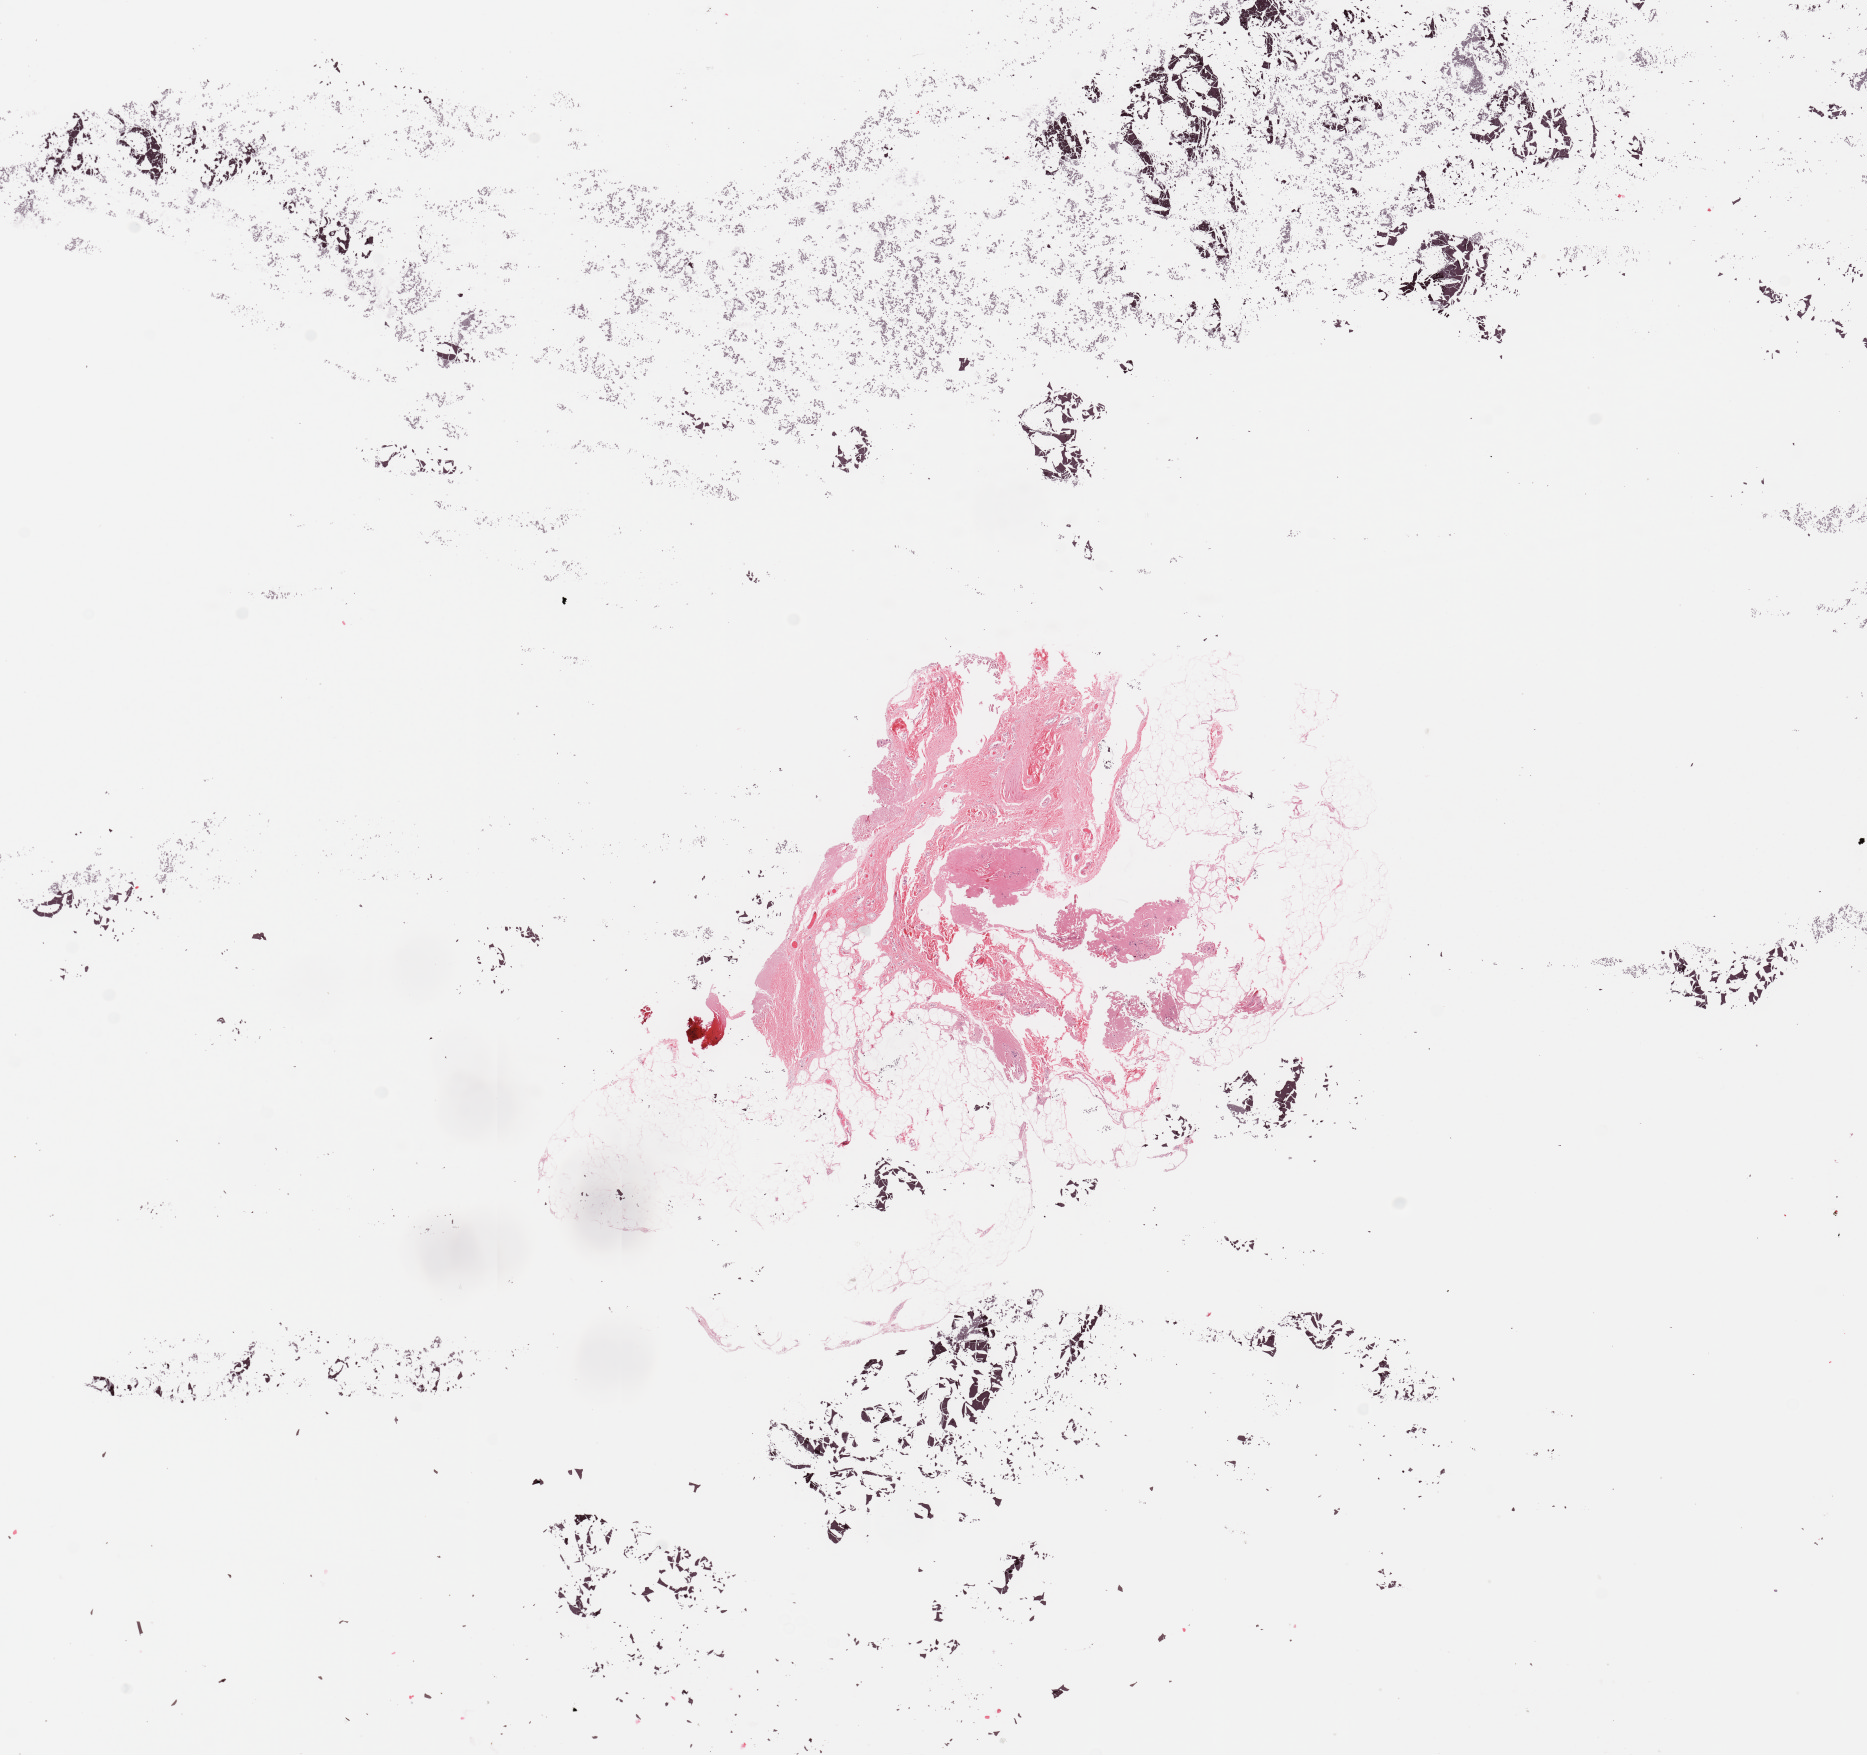
Digitized H&E-stained tissue section (whole slide) — a low-resolution overview of the entire scanned area, about 14.8 x 13.9 mm. Normal (non-tumour) tissue sample. Male, 67 y/o.
• this section: normal (non-tumour) tissue from the same patient
• patient diagnosis (cohort enrolment): sarcoma (site not recorded at cohort level)